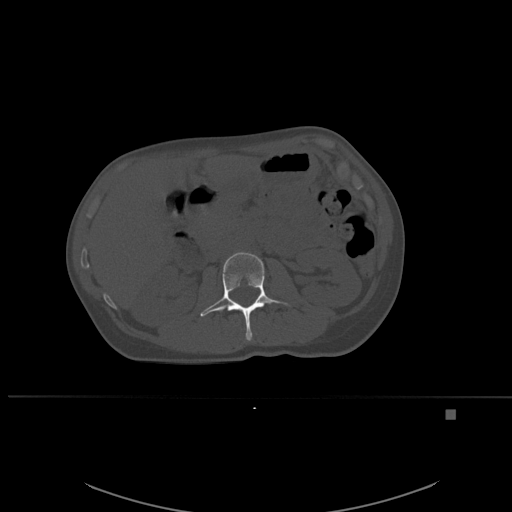
CT including the spine, one axial slice. Slice 237 of 537 in the series (ordered by position). Bone window (W 1800 / L 400 HU). 512 × 512 image matrix, field of view 440 × 440 mm. Patient: female, 45 years. Case-level facts recorded for this patient, not image findings: primary cancer: lung.
Structures marked on this image (semi-automatic segmentation, software-assisted and operator-edited):
- L2 vertebra: box from (x=200, y=252) to (x=290, y=341) px